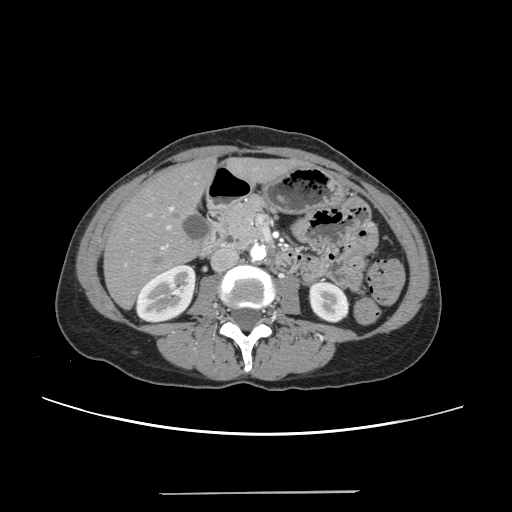
Contrast-enhanced abdominal CT, one axial slice; slice 92 of 240 in the series (ordered by position); intravenous contrast given; soft-tissue window (W 400 / L 40 HU); 1.25 mm slice thickness; 512 × 512 image matrix. Female patient, age 60 years. Case-level facts recorded for this patient, not image findings: diagnosis: colorectal cancer liver metastases, imaged before liver resection; multiple liver metastases: no; largest metastasis: 1.5 cm.
Outlined on this slice (manually delineated by an expert):
- liver: bounding box (x1, y1, x2, y2) in pixels: (106, 160, 292, 306)
- planned liver remnant (the part of the liver to remain after resection): (106, 161, 291, 306)
- portal vein (with intrahepatic branches): (124, 206, 173, 267)